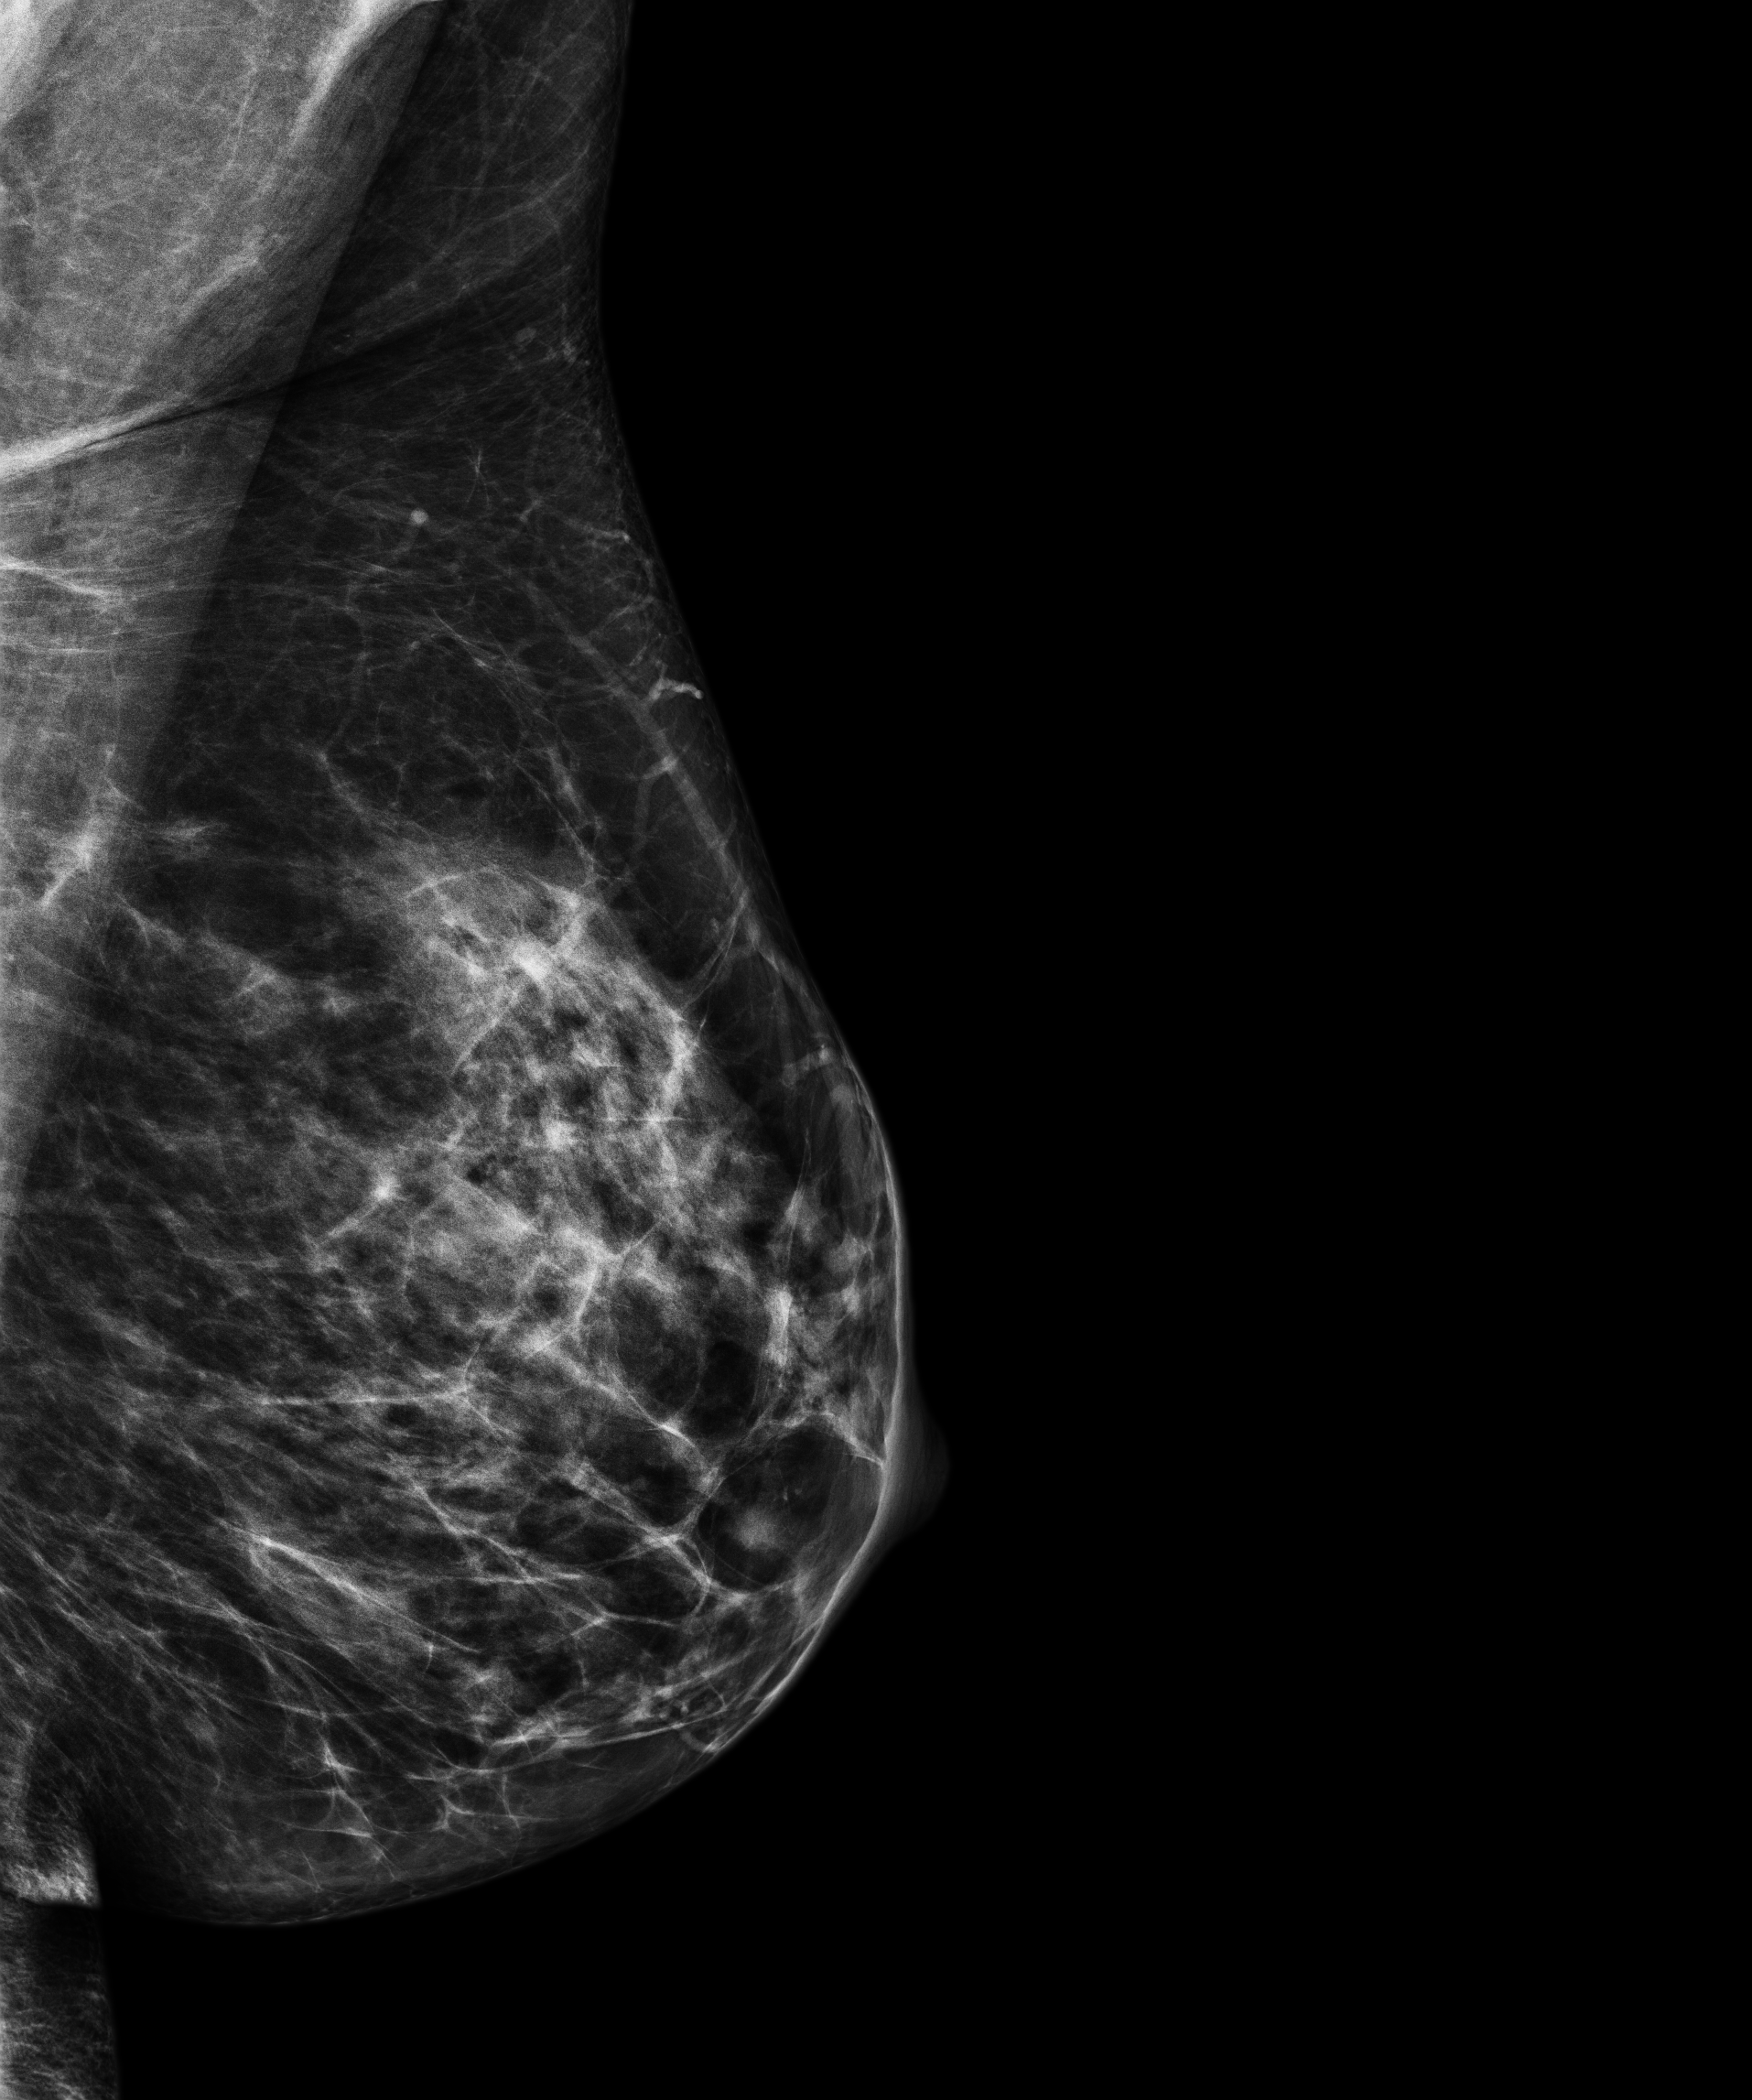
Annual screening mammography examination, compressed breast thickness 77.3 mm, system: Senographe Pristina. Patient aged 46 years (female).
Image type: full-field digital mammogram. Breast: left. Projection: mediolateral oblique (MLO) view.